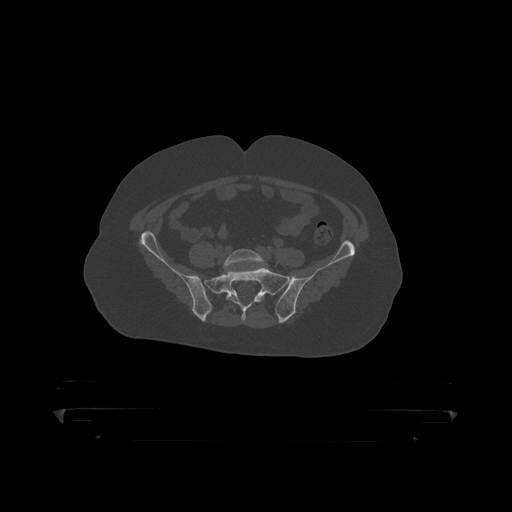
CT including the spine, one axial slice. Position 23 of 390 along the scan axis. 120 kVp. Bone window (W 1800 / L 400 HU). 1.25 mm slice thickness. 512 × 512 image matrix, field of view 650 × 650 mm. Male patient, age 60 years. Case-level facts recorded for this patient, not image findings: primary cancer: prostate.
Annotated regions visible in this slice (semi-automatically segmented with operator editing):
- L5 vertebra: bounding box [x1, y1, x2, y2] px = [223, 249, 266, 293]